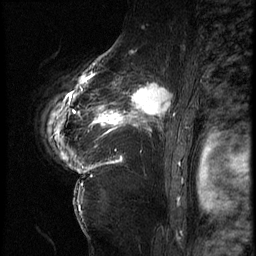
Breast MRI (dynamic contrast-enhanced), one sagittal slice; 3 images stored at this slice position (order not interpretable as contrast timing); 1.5 T; TE 4.2 ms, TR 9 ms; 256 × 256 image matrix, field of view 180 × 180 mm. Patient: female, 56 years. Case-level facts recorded for this patient, not image findings: setting: breast cancer imaged before/during neoadjuvant chemotherapy; receptor status: HER2-positive.
Outlined on this slice (semi-automatically segmented with operator editing):
- analysis volume of interest (the breast-tissue region the enhancement analysis was run in; not a lesion): box from (x=84, y=75) to (x=181, y=153) px
- tumour enhancement mask (voxels above the 140 % enhancement threshold inside the analysis volume of interest): (x=84, y=75)–(x=173, y=137)